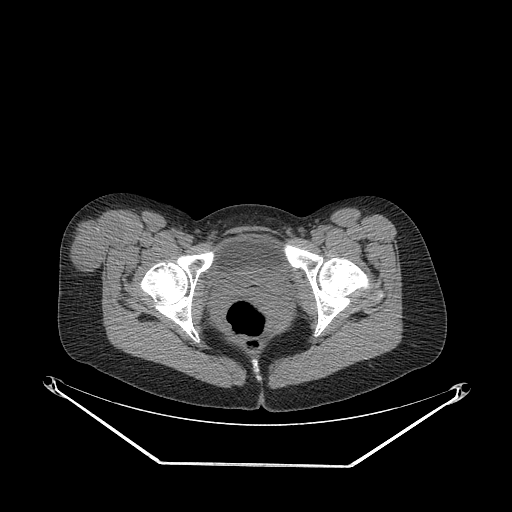
CT of an extremity soft-tissue mass (from a PET/CT study), one axial slice. Slice 65 of 267 in the series (ordered by position). Reconstruction kernel STANDARD. 140 kVp. Soft-tissue window (W 400 / L 40 HU). 3.75 mm slice thickness. 512 × 512 image matrix, field of view 500 × 500 mm. Female patient. From the clinical record (not read from this slice): histological type: synovial sarcoma; grade: intermediate; site of the primary tumour: right thigh.
Annotated regions visible in this slice (expert contour drawn on MRI and transferred to this co-registered scan by the dataset authors):
- gross tumour volume including surrounding oedema: bounding box [x1, y1, x2, y2] px = [69, 217, 122, 275]
- gross tumour volume (mass): [69, 217, 122, 273]